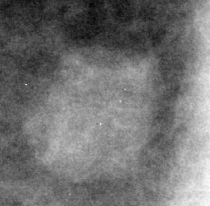
Region of interest cut from a scanned film mammogram (one marked finding); right breast; CC view; BI-RADS breast density category 2 (scale 1–4).
- Finding: mass, shape lobulated, margins circumscribed; BI-RADS assessment category 4; pathology (as recorded): benign.